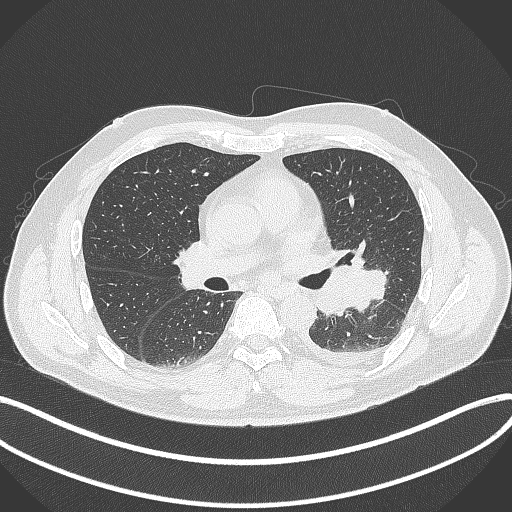
Chest CT, one axial slice; position 198 of 342 along the scan axis; reconstruction kernel B70f; 120 kVp; lung window (W 1500 / L -600 HU); 1 mm slice thickness; 512 × 512 image matrix, field of view 400 × 400 mm. Patient: male, 58 years. Case-level facts recorded for this patient, not image findings: clinical TNM (as recorded): T3 N1 M1b.
Outlined on this slice (bounding box drawn by a radiologist):
- lung tumour (recorded histology: small cell carcinoma): bounding box <316,260,393,319> (left, top, right, bottom; pixels)